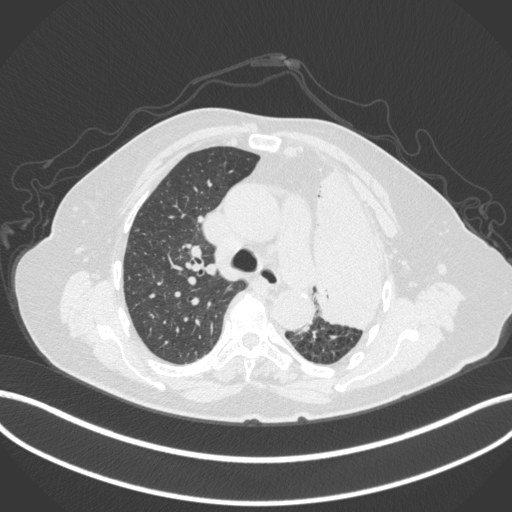
Chest CT, one axial slice; slice 267 of 399 in the series (ordered by position); reconstruction kernel B31f; 120 kVp; lung window (W 1500 / L -600 HU); 512 × 512 image matrix, field of view 400 × 400 mm. Patient: female, 75 years. From the clinical record (not read from this slice): clinical TNM (as recorded): T3 N3 M1.
Annotated regions visible in this slice (rectangle marked by the reading radiologist):
- lung tumour (recorded histology: adenocarcinoma): box from (x=305, y=159) to (x=399, y=338) px